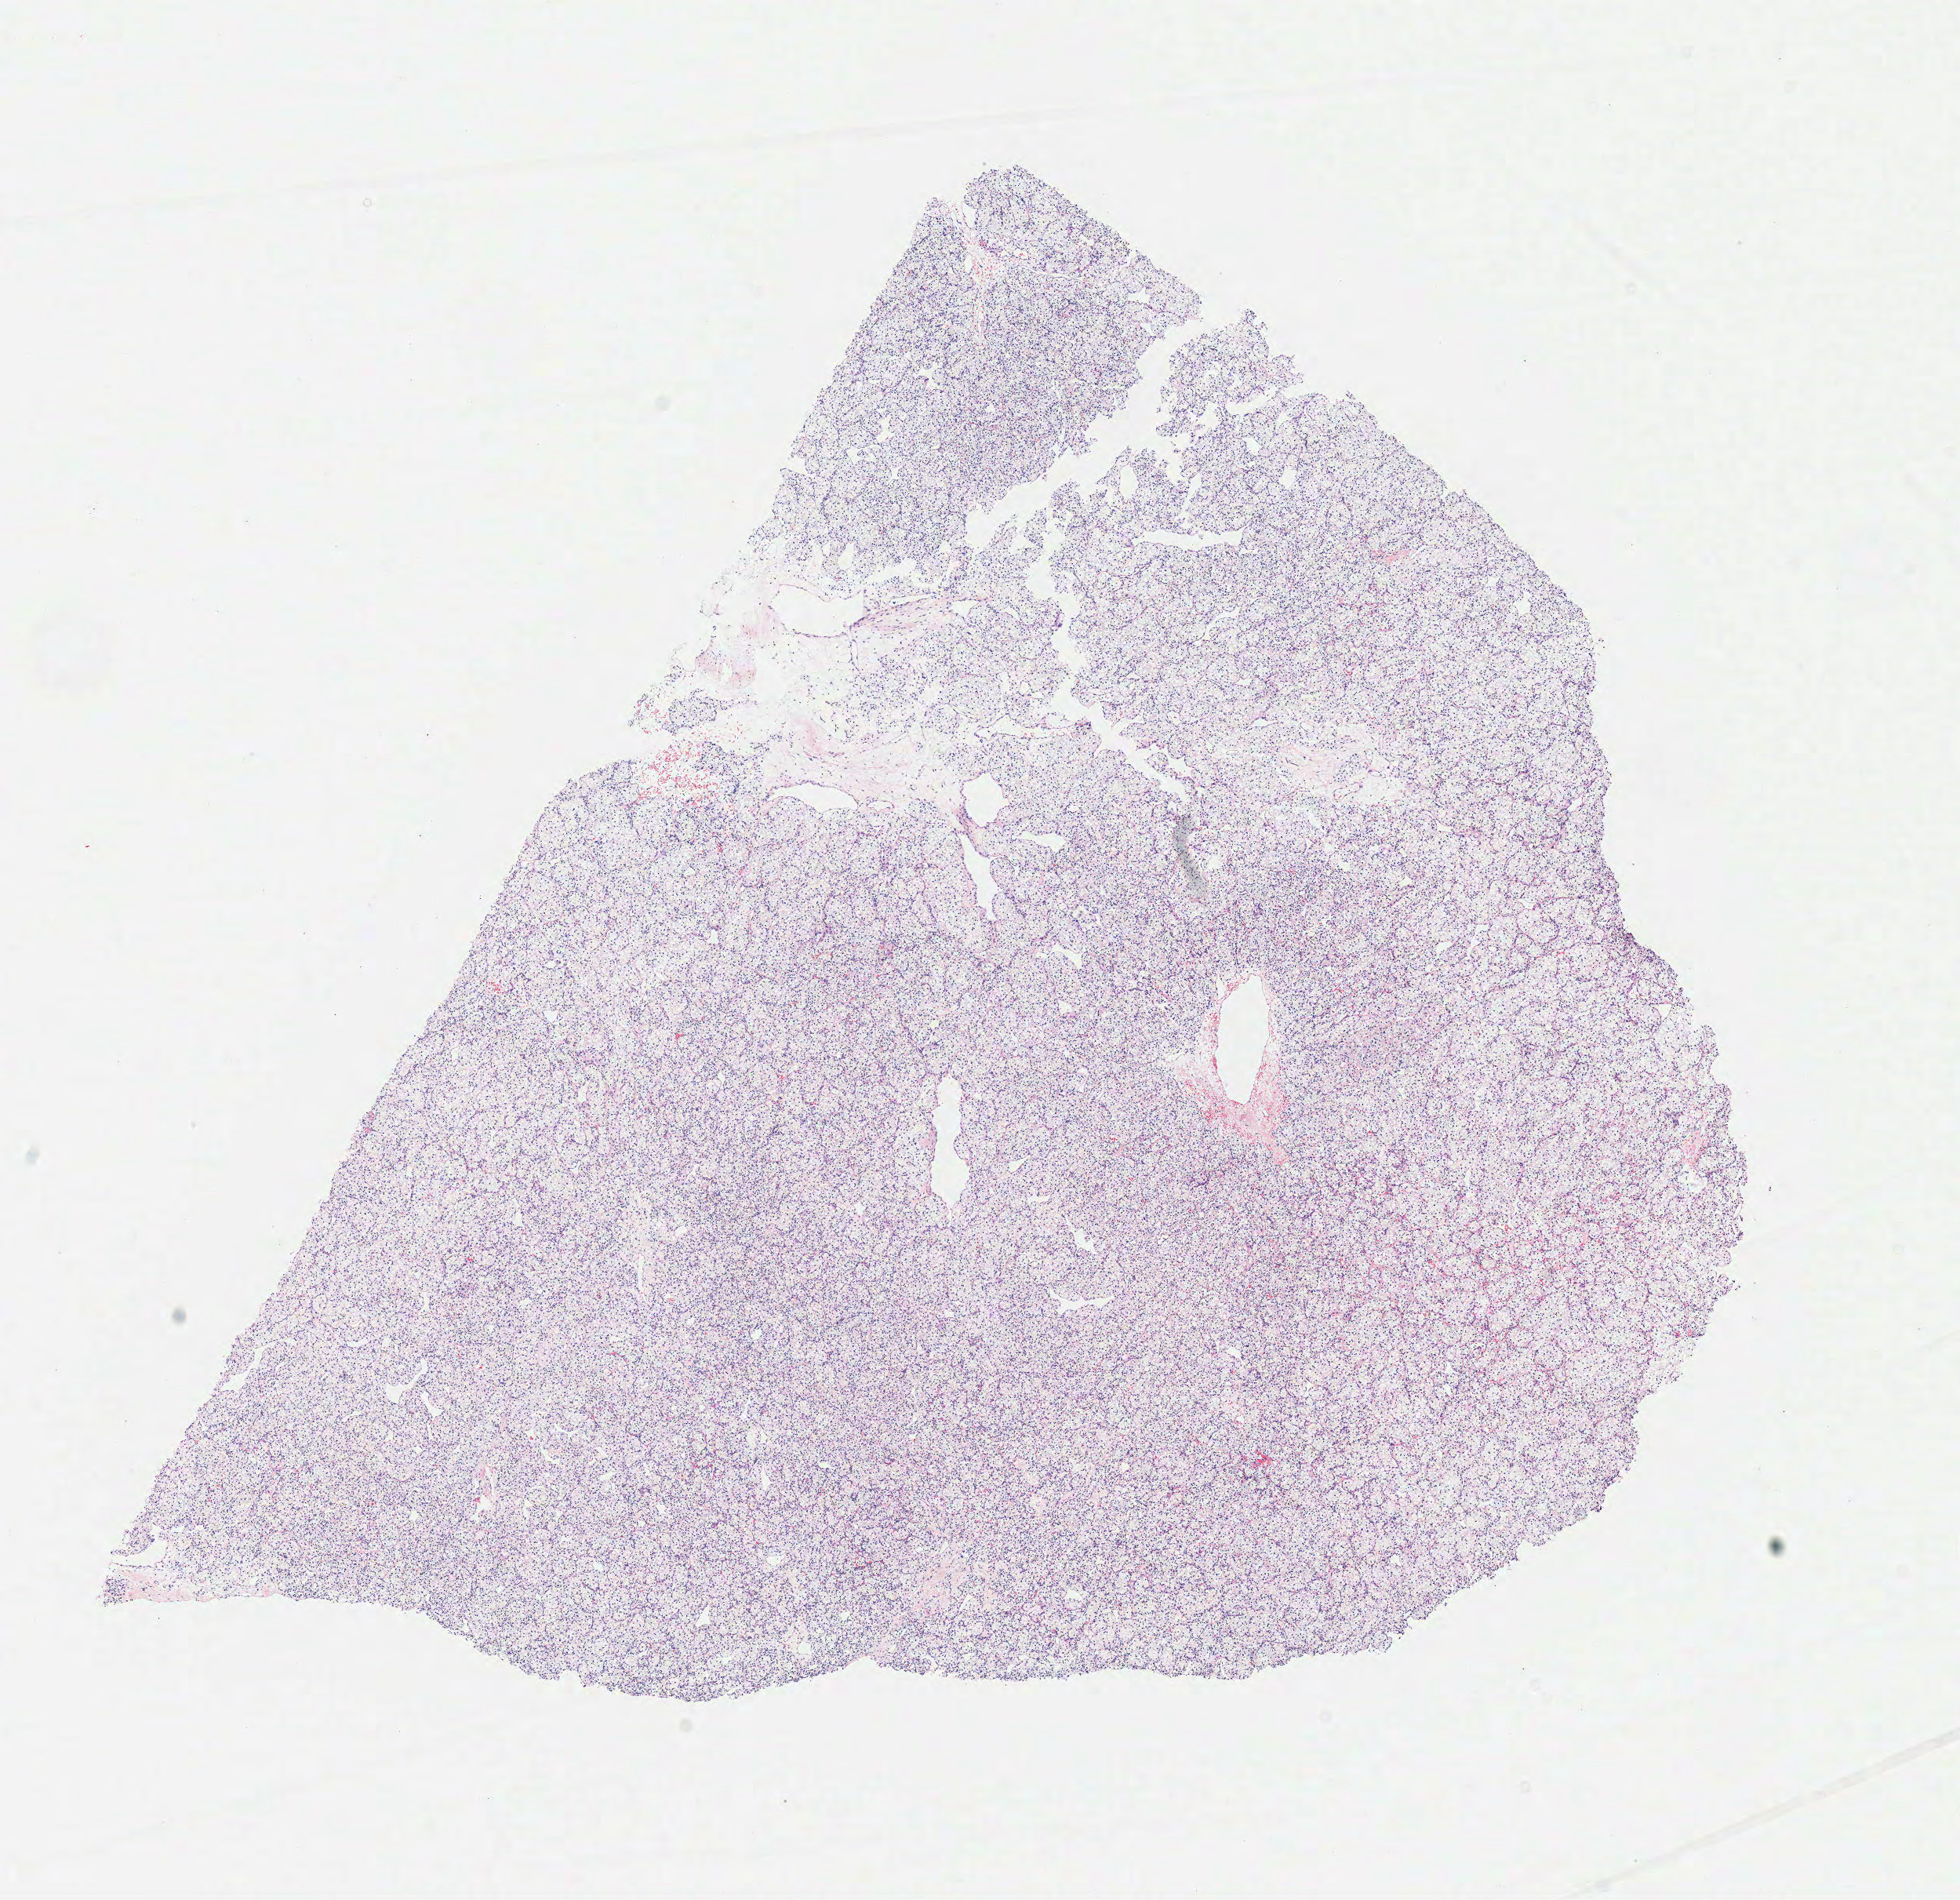
Whole-slide histology image, Hematoxylin and eosin (H&E) stained, whole scanned area (about 9.8 x 9.5 mm) shown as a low-resolution overview, frozen section, sample: primary tumour, kidney. Patient: female, age at initial diagnosis 47 years. Histologic grade: G1 (well differentiated). Pathologist review of this section (percent, as recorded): tumour cells 95%, tumour nuclei 90%, normal cells 0%, stromal cells 5%, necrosis 0%.
AJCC pathologic stage: I. Diagnosis: Clear cell adenocarcinoma, NOS.